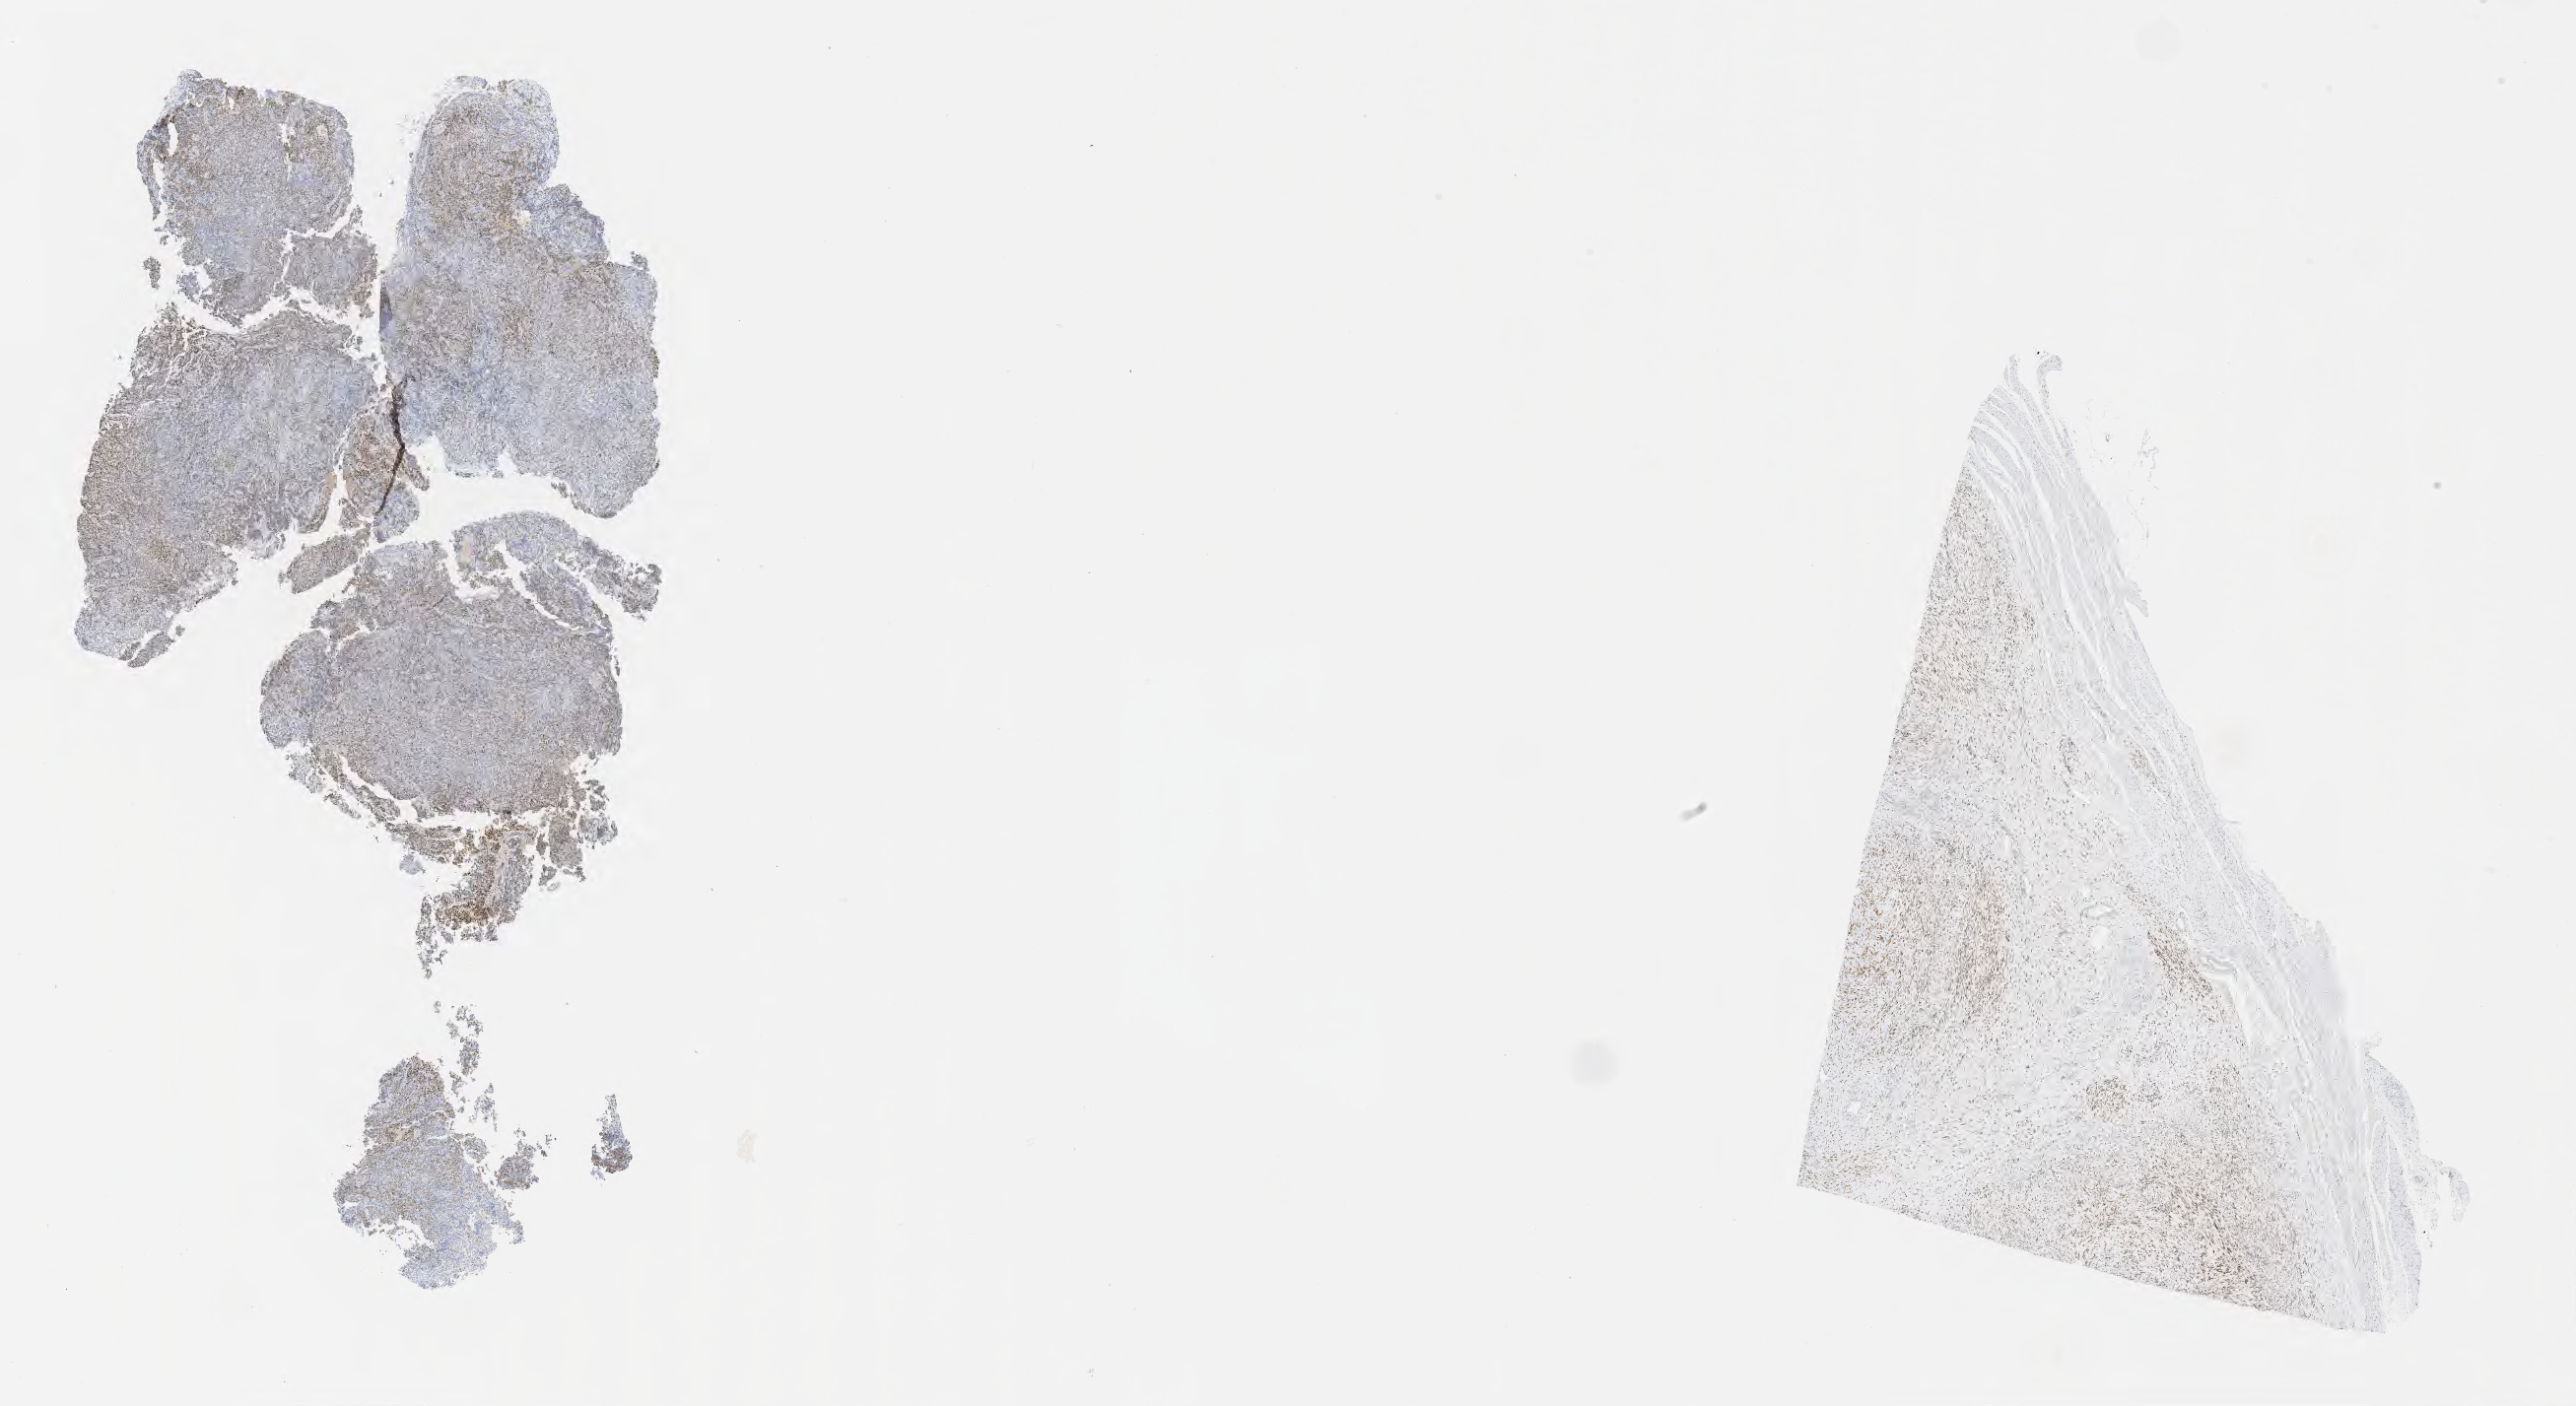
Whole-slide image, immunohistochemical stain for estrogen receptor (ER) — low-resolution overview of the scanned area, about 21.1 x 11.5 mm. Specimen: tumor tissue. Anatomic site: cervix. Patient female; age 75 years.
Diagnosis: Adenocarcinoma, NOS.